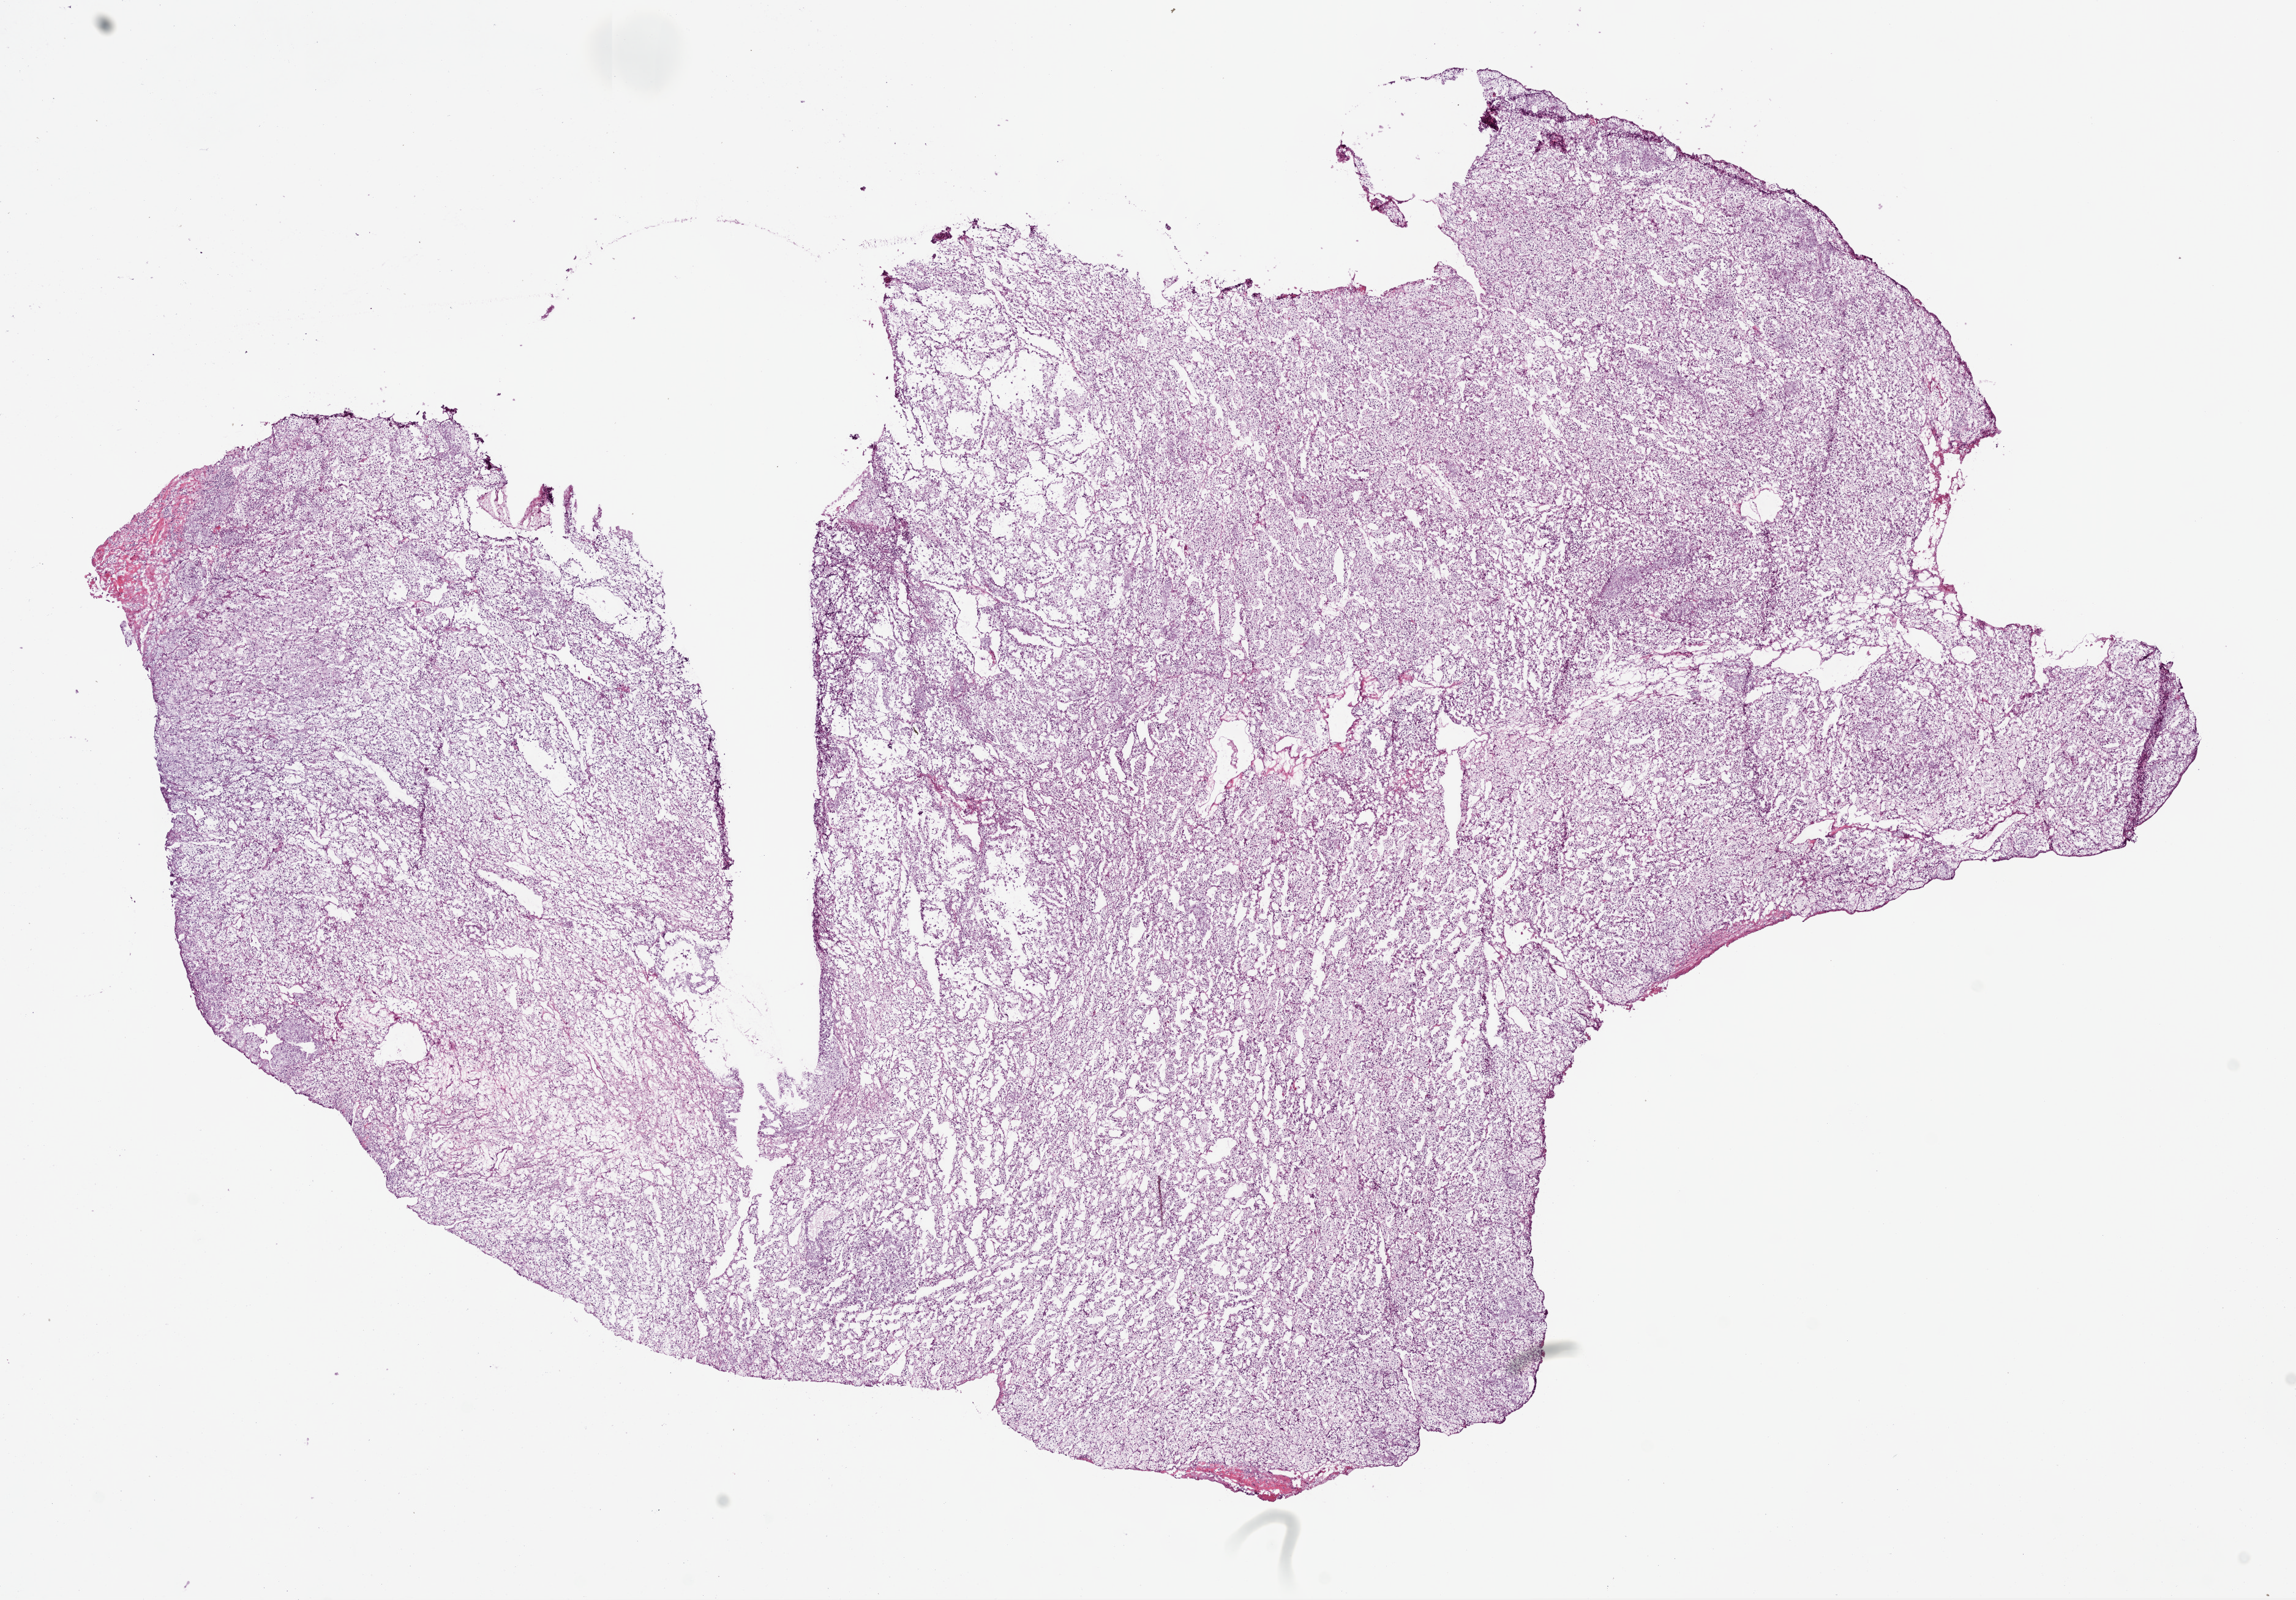
H&E whole-slide image, whole scanned area (about 15.0 x 10.5 mm) shown as a low-resolution overview; frozen section; sample: primary tumour, kidney. Patient: male, age at initial diagnosis 63 years. Histologic grade: G4 (undifferentiated). Composition of this section per pathologist review: tumour cells 95%, tumour nuclei 90%, normal cells 0%, stromal cells 5%, necrosis 0%. Infiltration values recorded for this section: lymphocyte infiltration 2%, monocyte infiltration 0%, neutrophil infiltration 0%.
* diagnosis: Clear cell adenocarcinoma, NOS
* AJCC pathologic stage: IV (6th edition)